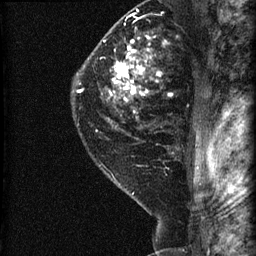
Breast MRI (dynamic contrast-enhanced), one sagittal slice; dynamic contrast-enhanced series, image 2 of 3 at this slice position (ordered by acquisition); 1.5 T; TE 4.2 ms, TR 22.7 ms; 1.8 mm slice thickness; 256 × 256 image matrix, field of view 180 × 180 mm. Female patient, age 45 years. From the clinical record (not read from this slice): setting: breast cancer imaged before/during neoadjuvant chemotherapy; receptor status: HR-positive, HER2-negative.
Annotated regions visible in this slice (semi-automatic segmentation, software-assisted and operator-edited):
- analysis volume of interest (the breast-tissue region the enhancement analysis was run in; not a lesion): box from (x=74, y=11) to (x=205, y=140) px
- tumour enhancement mask (voxels above the 90 % enhancement threshold inside the analysis volume of interest): (x=77, y=40)–(x=160, y=101)